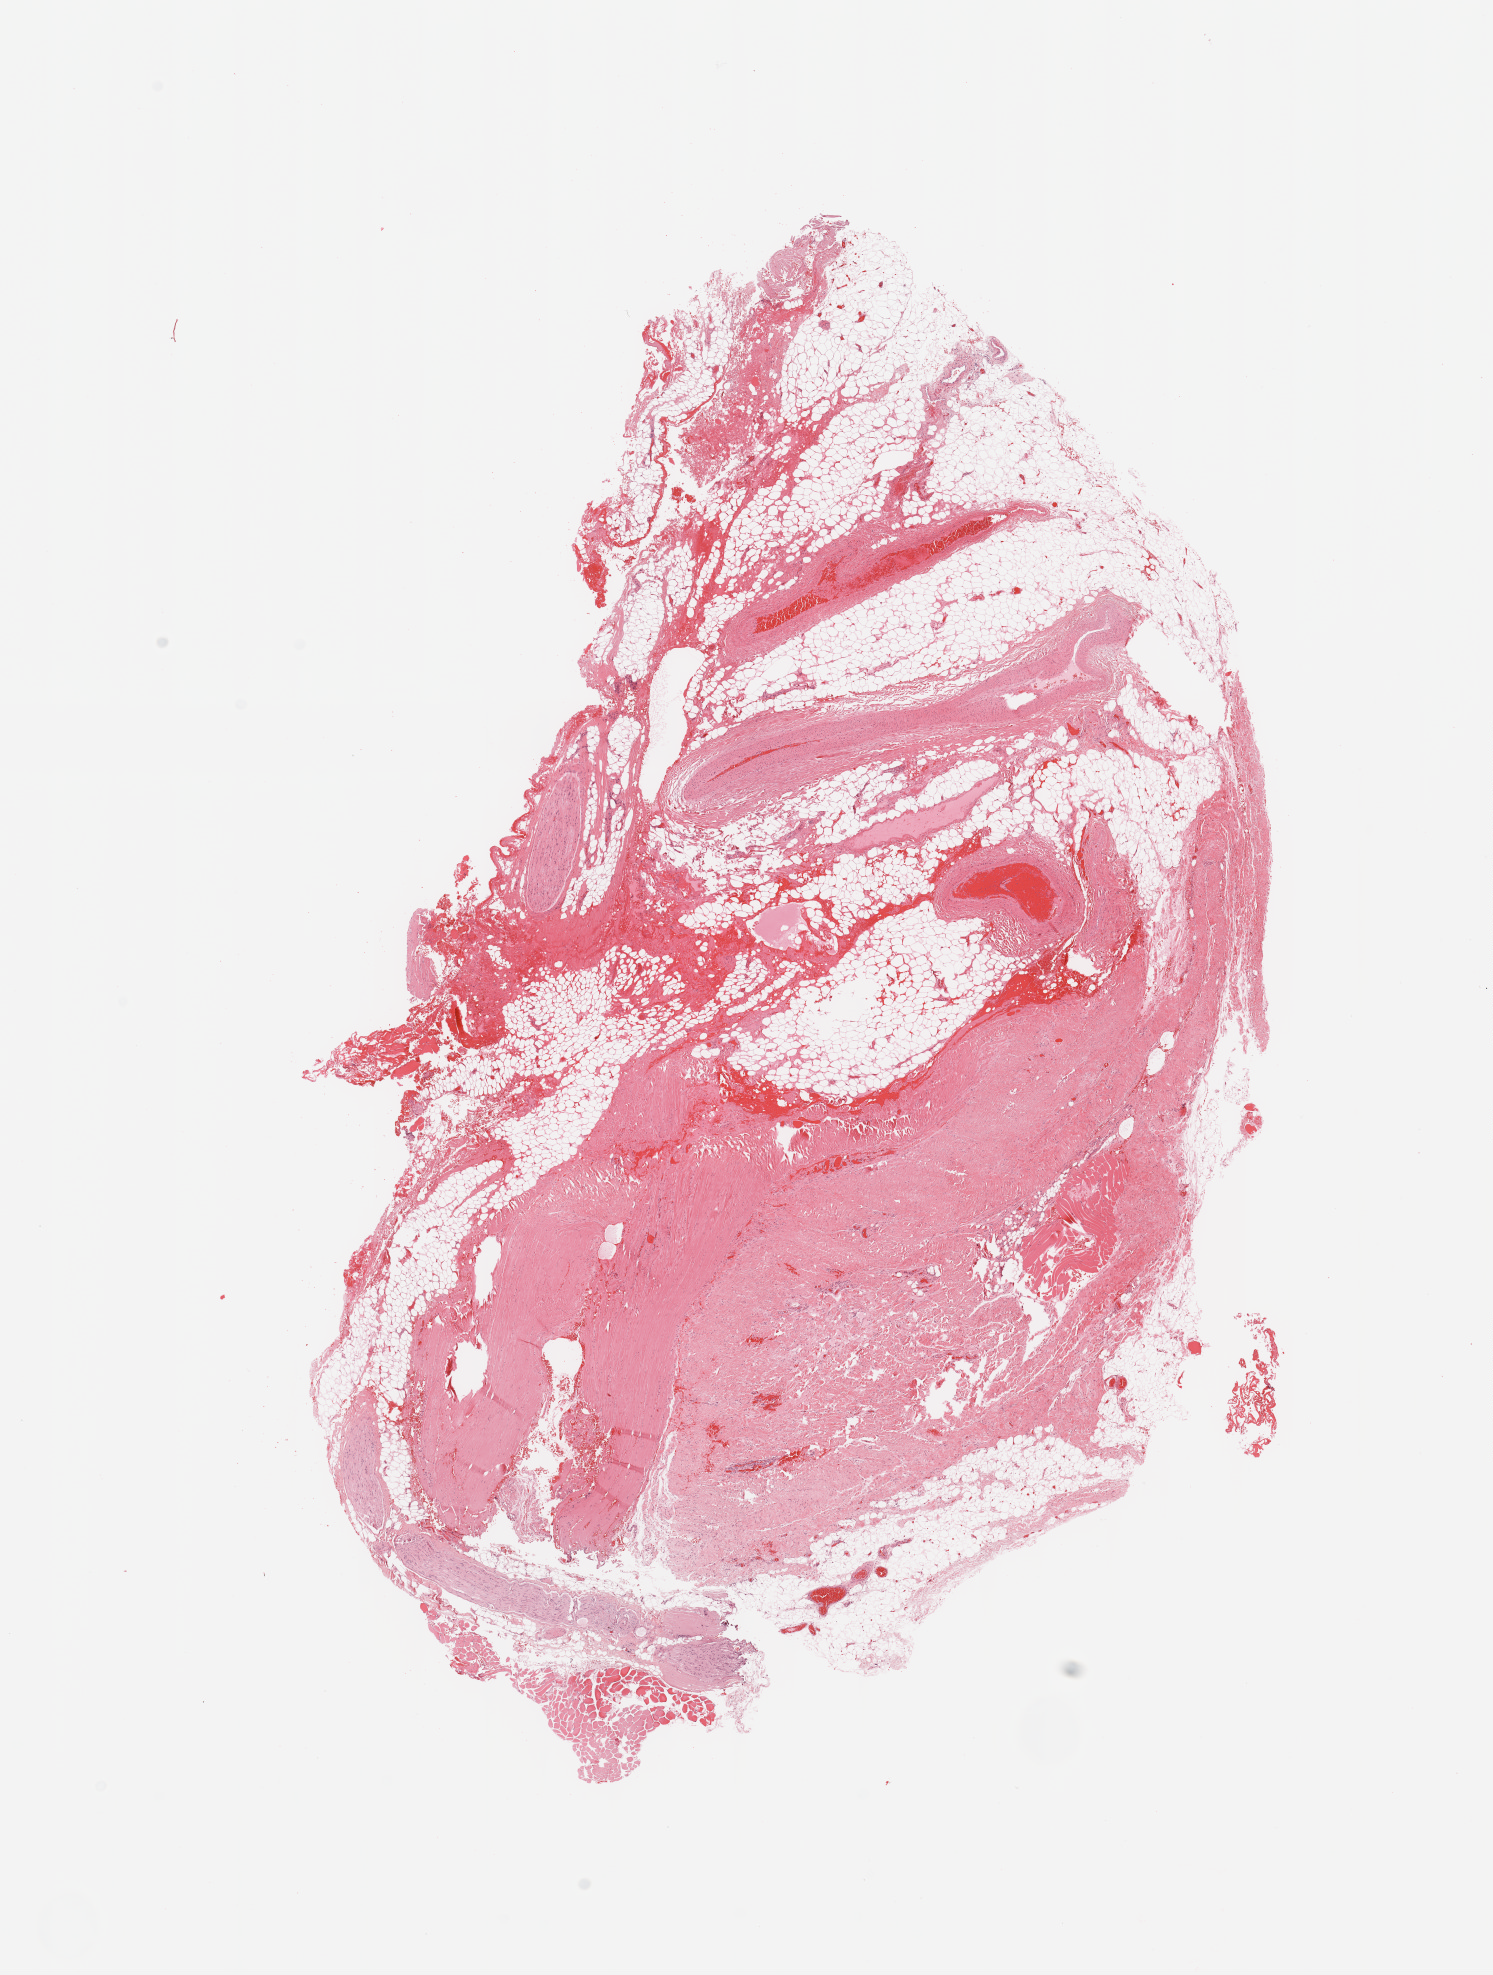
Hematoxylin and eosin (H&E) stained whole-slide image — low-resolution overview of the scanned area, about 11.8 x 15.6 mm (slide scanned at 20x). Male, 66 y/o.
- patient diagnosis (cohort enrolment): sarcoma (site not recorded at cohort level)
- primary tumour site (as recorded): pelvic